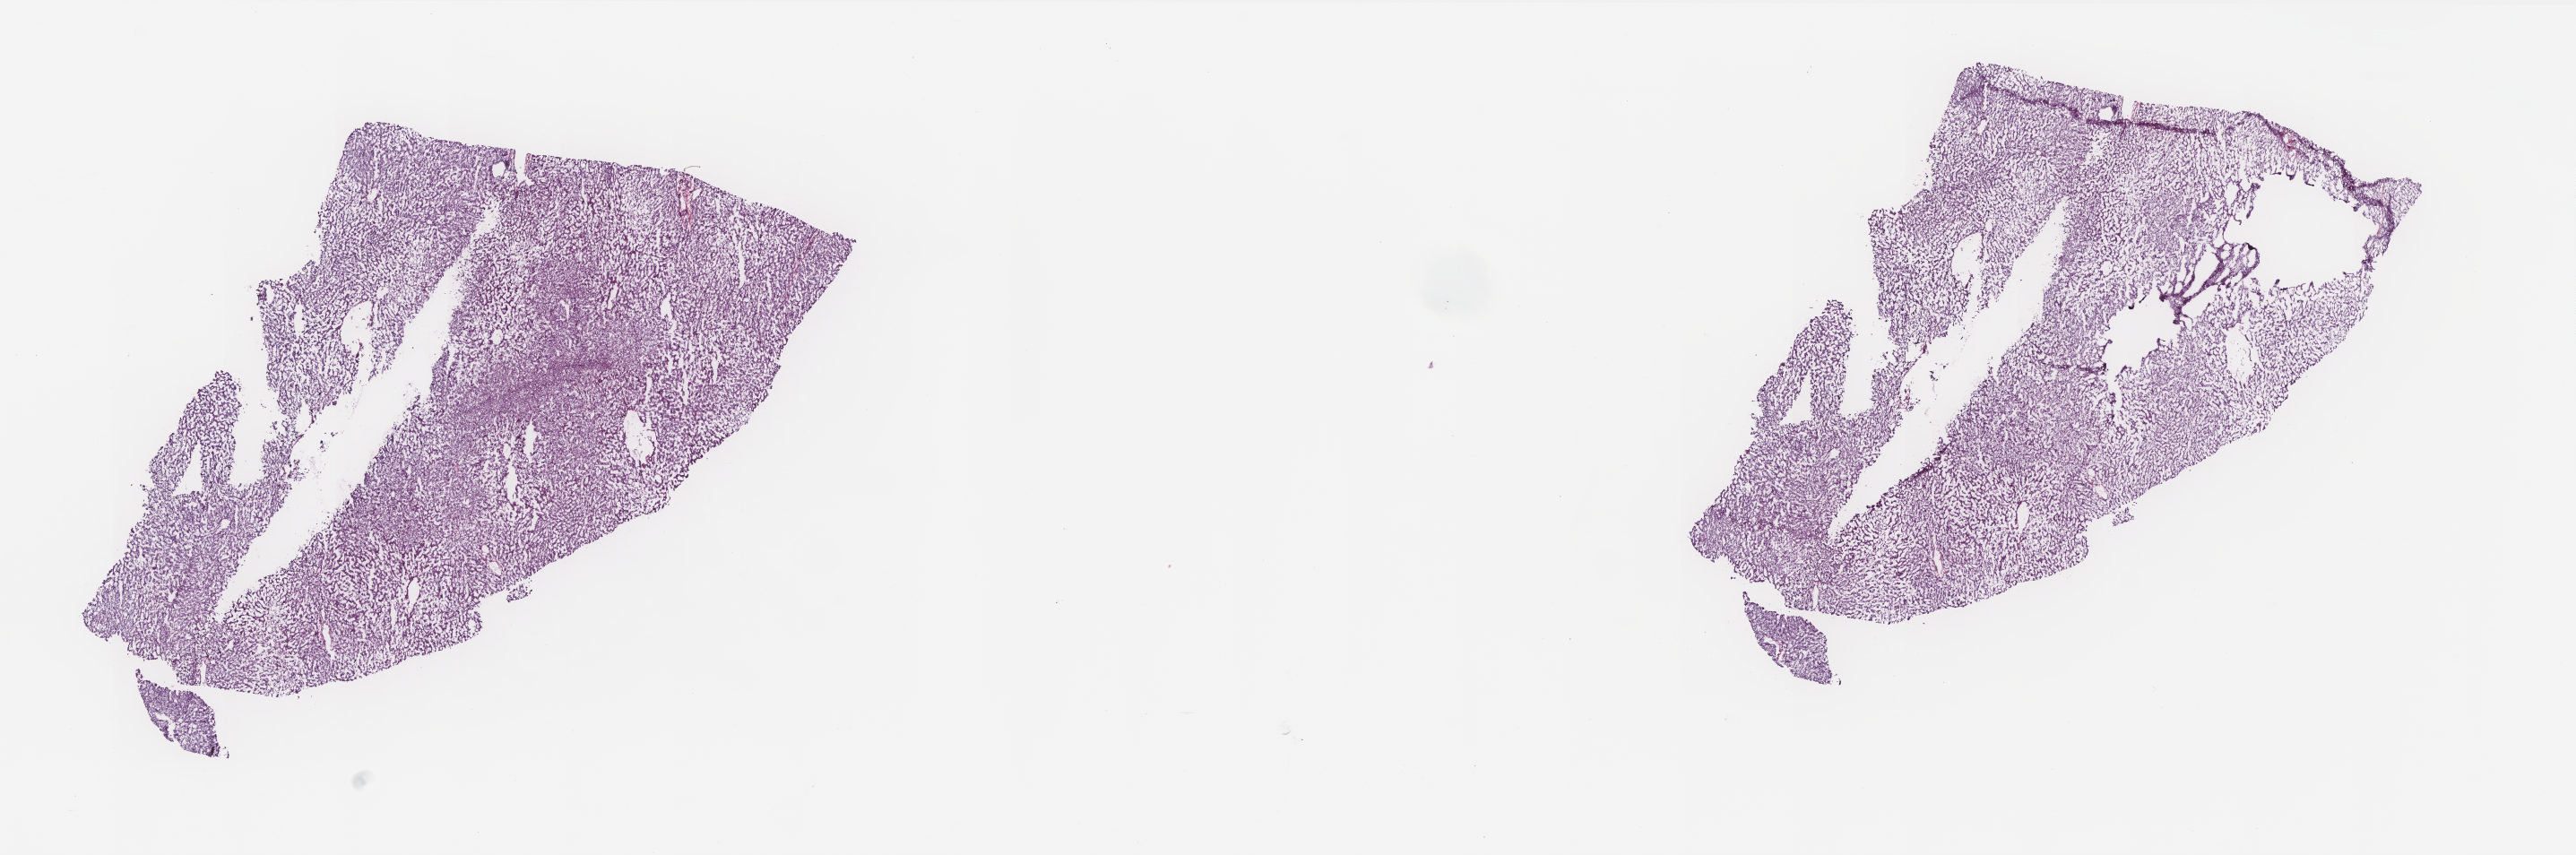
Digitized Hematoxylin and eosin (H&E) stained tissue section (whole slide), low-resolution overview of the scanned area, about 23.0 x 7.6 mm (acquisition: 20x scan); frozen section from the top of the tissue portion; liver, solid tissue normal (non-tumour tissue) sample. Male, age 67 years at initial diagnosis. Pathologist review of this section (percent, as recorded): tumour cells 0%, tumour nuclei 0%, normal cells 90%, stromal cells 10%, necrosis 0%. Infiltration values recorded for this section: lymphocyte infiltration 1%, monocyte infiltration 0%, neutrophil infiltration 0%.
* this section: solid tissue normal sample (biorepository sample class)
* patient diagnosis: Hepatocellular carcinoma, NOS